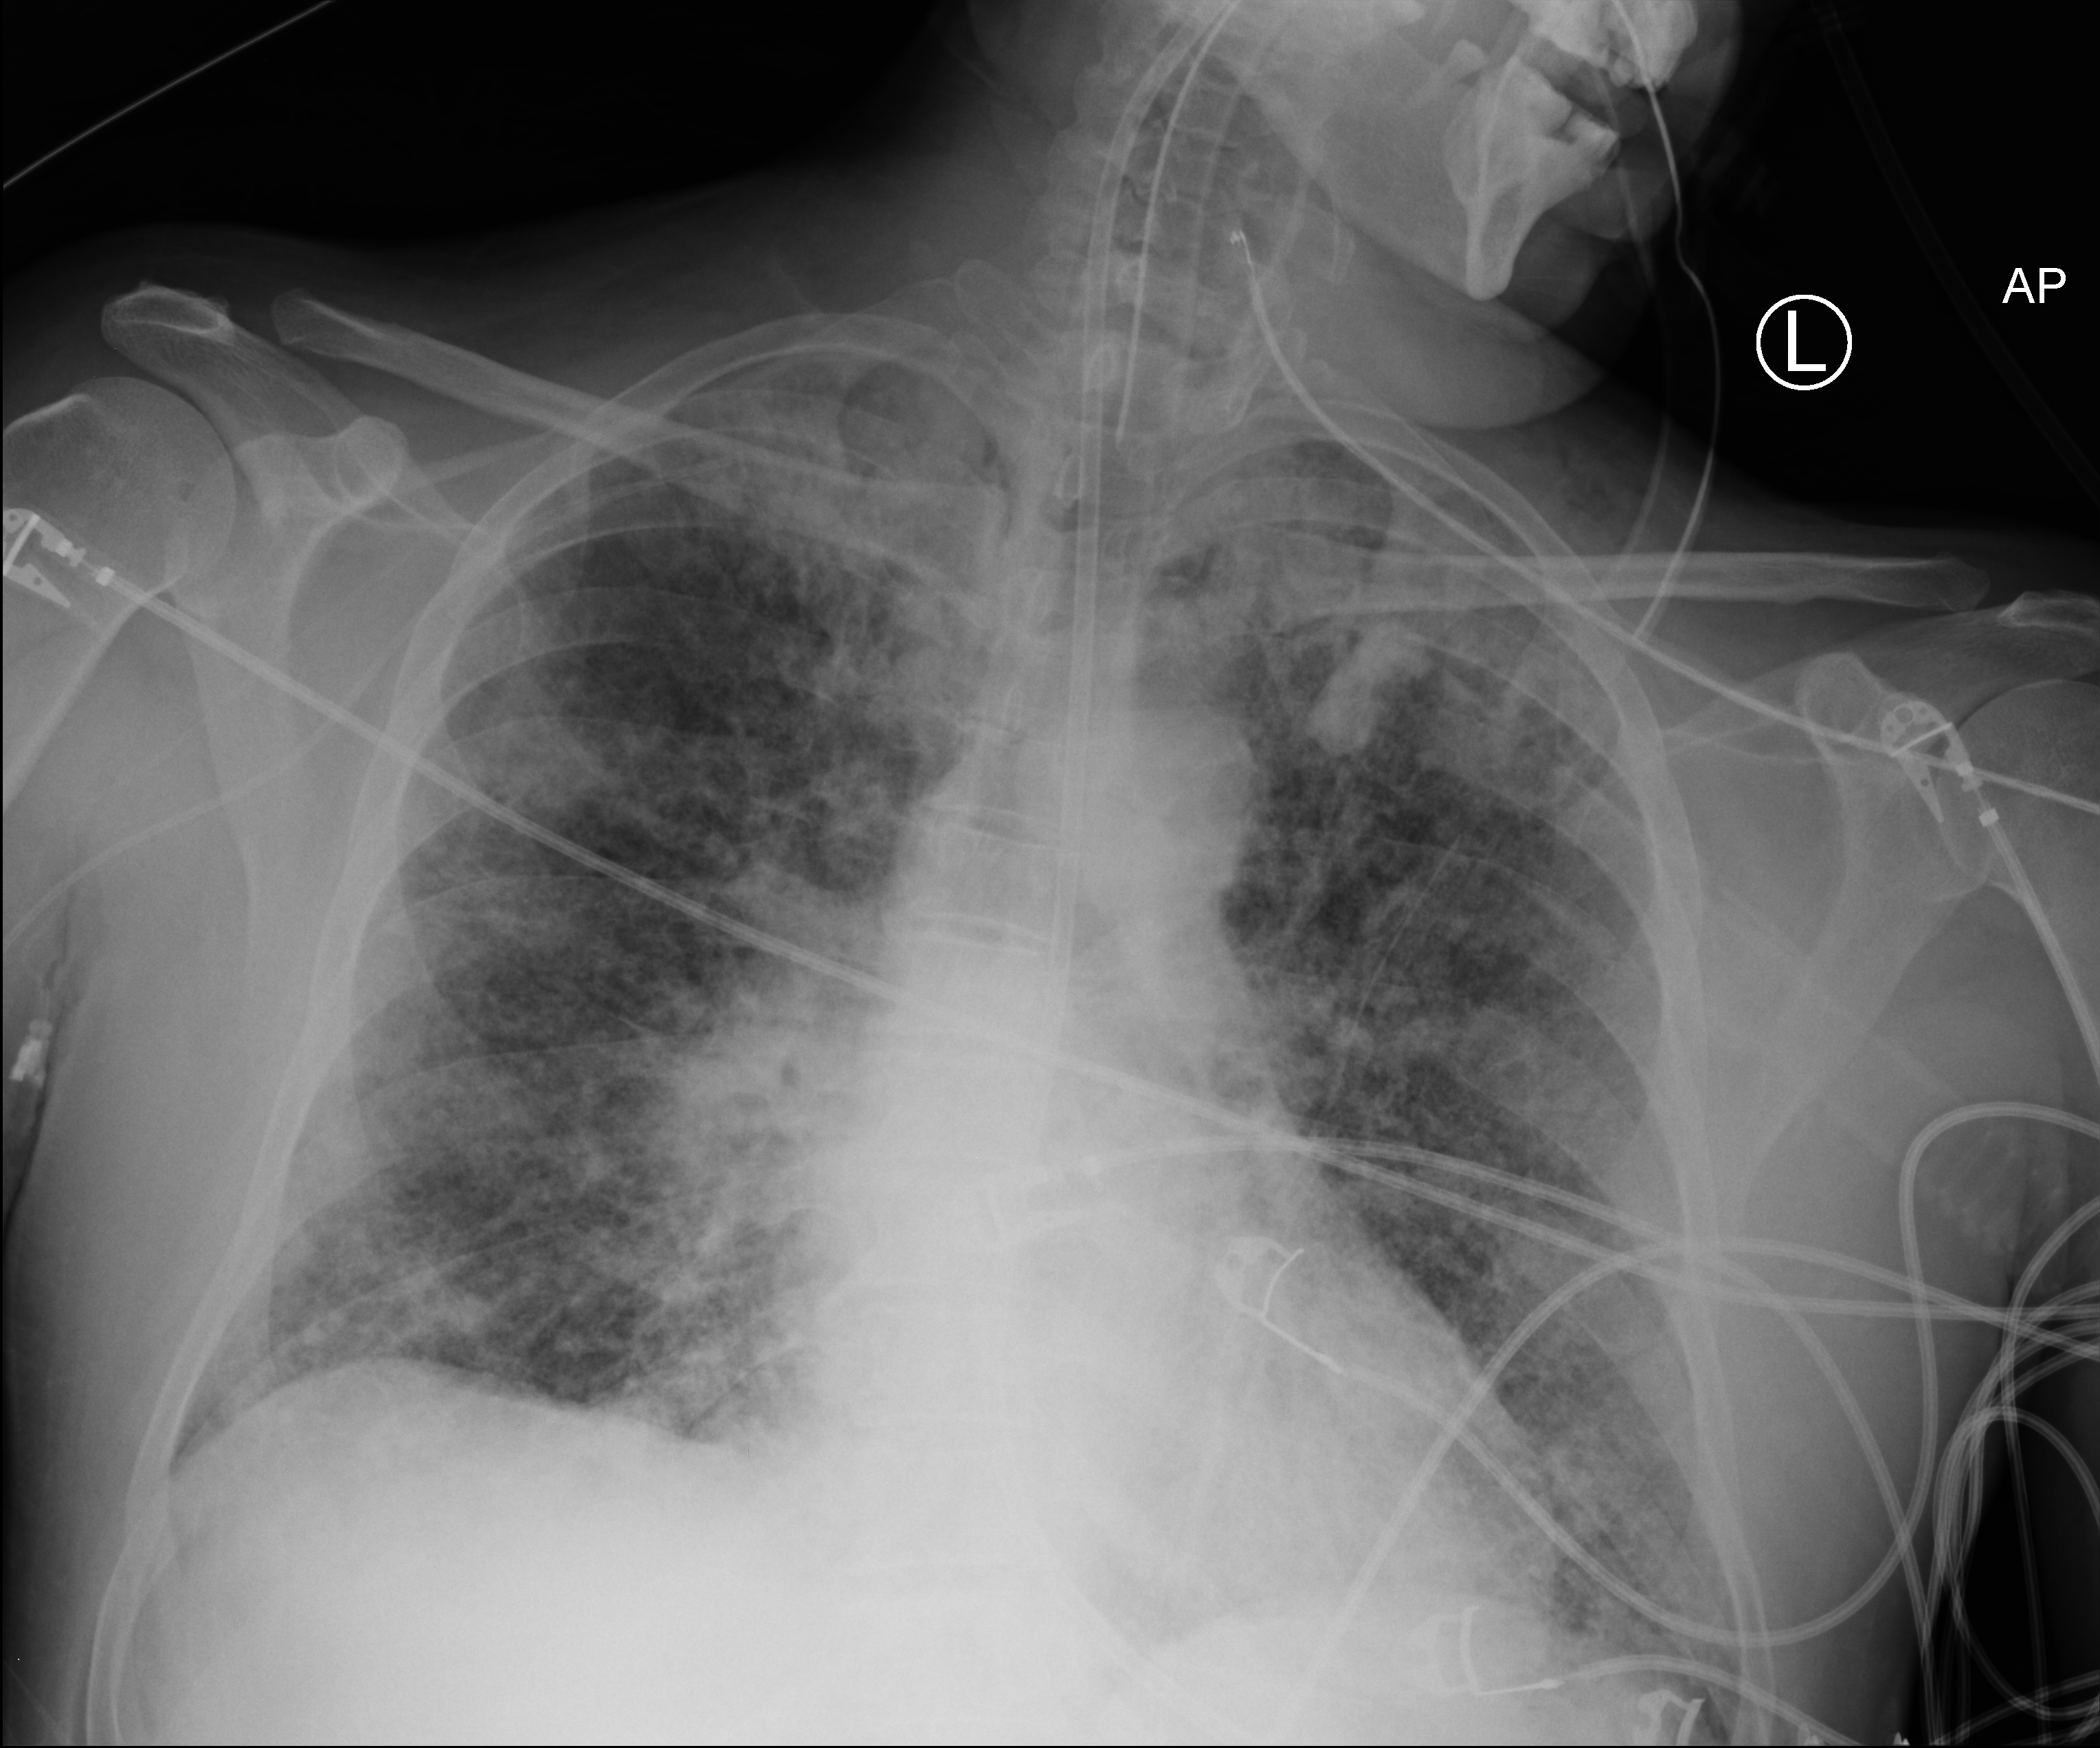
Chest X-ray (portable). Patient hospitalised with COVID-19; male, aged 18–59 years.
From the hospital-stay record, not from the radiograph (when in the stay this image was taken is not recorded): mechanically ventilated during this hospital stay: yes.